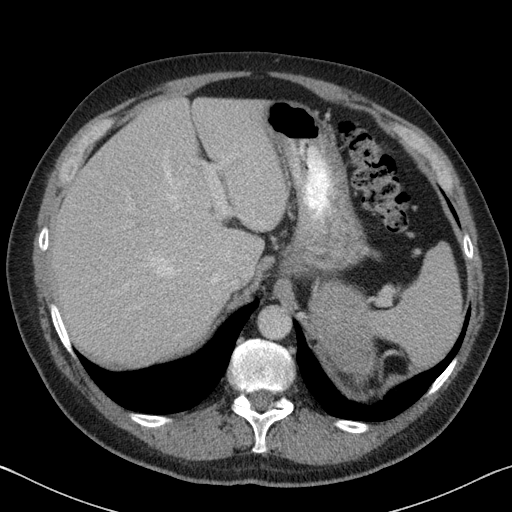
Contrast-enhanced abdominal CT, one axial slice; slice 63 of 88 in the series (ordered by position); intravenous contrast given; soft-tissue window (W 400 / L 40 HU); 3 mm slice thickness; 512 × 512 image matrix, field of view 366 × 366 mm. Patient: male, 51 years. Case-level facts recorded for this patient, not image findings: diagnosis: adrenocortical carcinoma; tumour side: left adrenal; tumour size at pathology: 16.5 cm.
Structures marked on this image (semi-automatic segmentation, software-assisted and operator-edited):
- mass: bounding box [x1, y1, x2, y2] px = [313, 287, 373, 373]